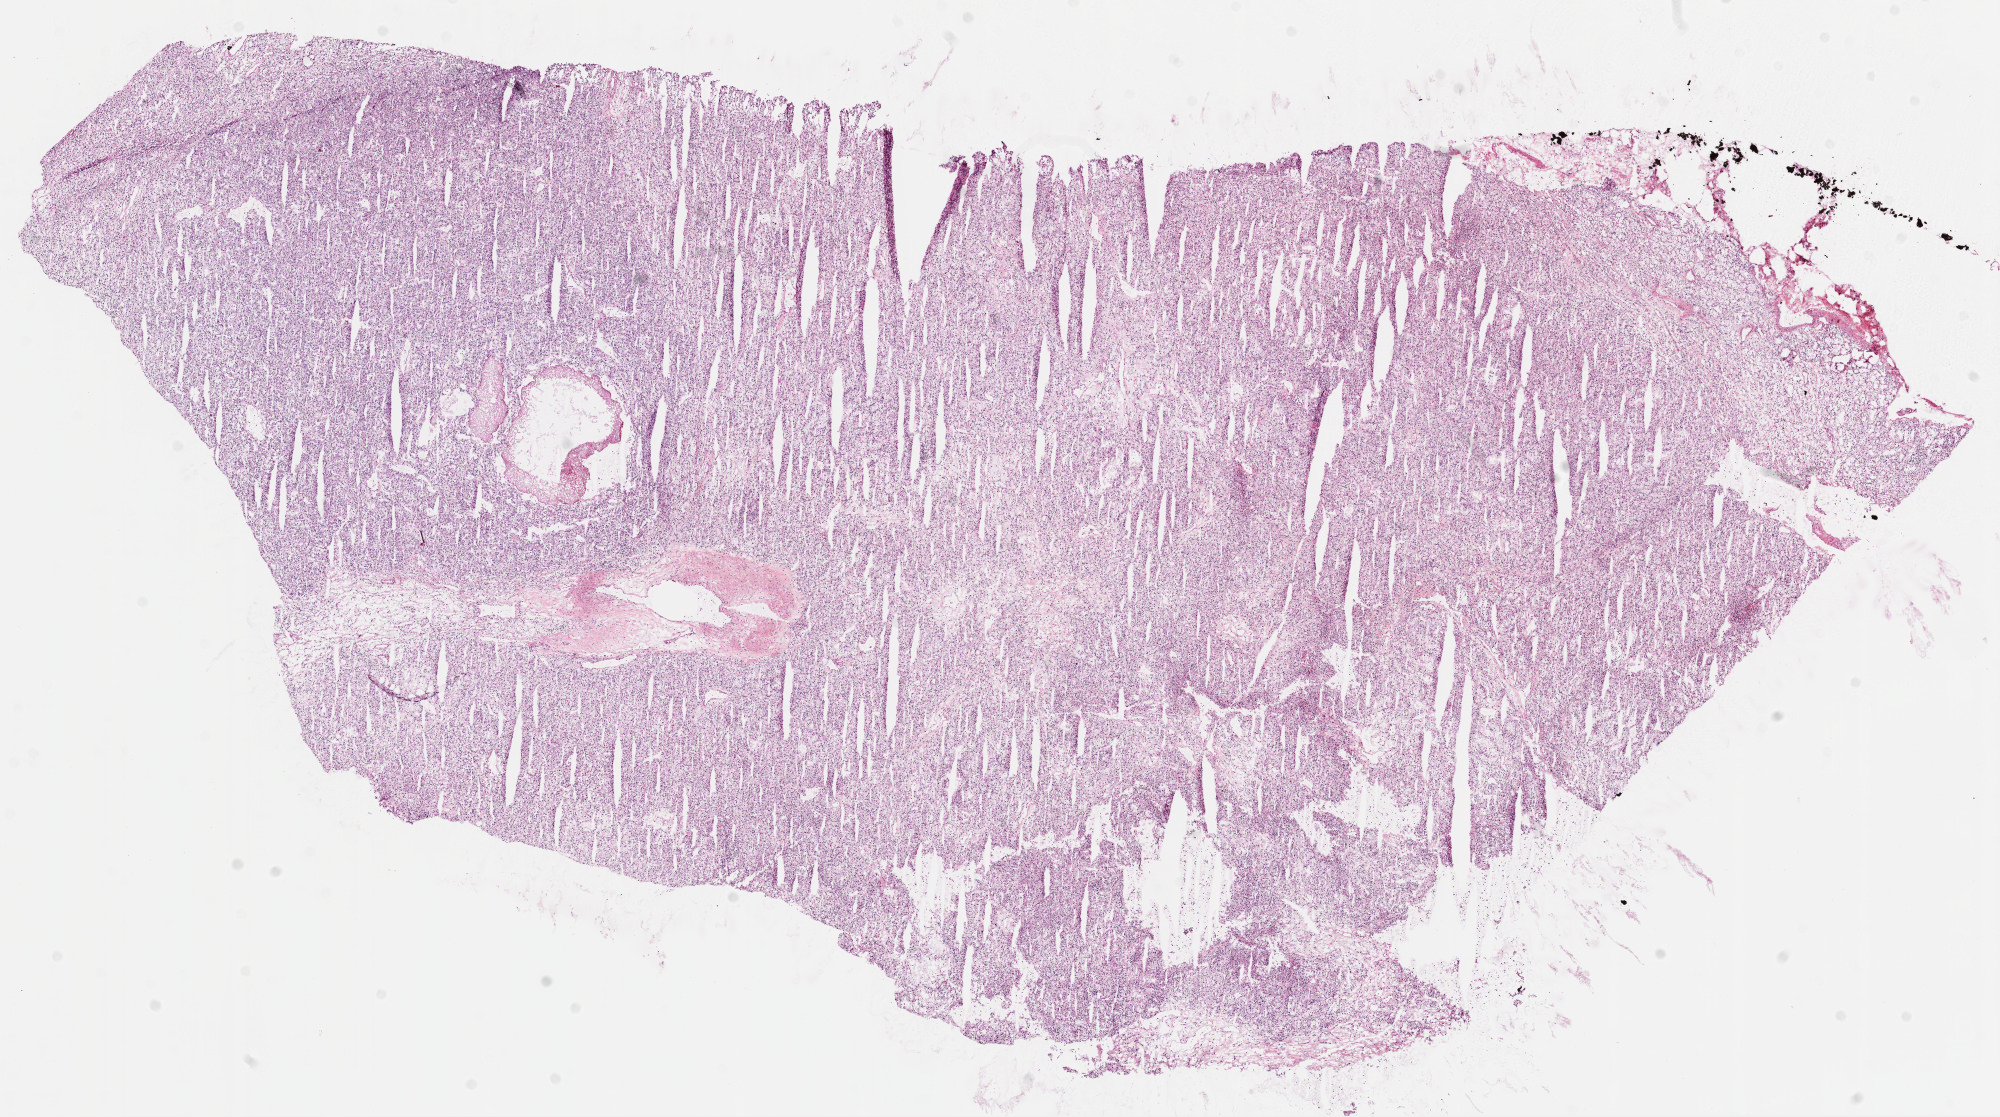
H&E whole-slide image — a low-resolution overview of the entire scanned area, about 16.0 x 9.0 mm (slide scanned at 20x); frozen section; sample: primary tumour, kidney. Female, age 61 years at initial diagnosis. Histologic grade: G2 (moderately differentiated). Slide review estimates, as recorded: tumour cells 100%, tumour nuclei 90%, normal cells 0%, stromal cells 0%, necrosis 0%. Inflammatory infiltration, as recorded: lymphocyte infiltration 2%, monocyte infiltration 0%, neutrophil infiltration 0%.
* AJCC pathologic stage: I
* lymph nodes positive (case pathology): 0 of 2 examined
* histologic diagnosis: Clear cell adenocarcinoma, NOS
* TNM: T1b N0 M0